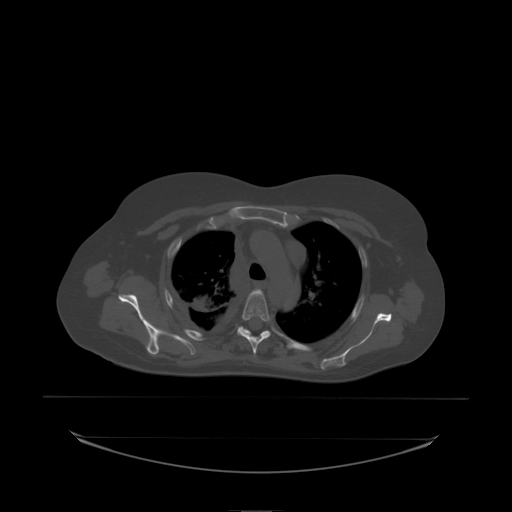
CT including the spine, one axial slice. Position 165 of 242 along the scan axis. Bone window (W 1800 / L 400 HU). 2.5 mm slice thickness. 512 × 512 image matrix, field of view 500 × 500 mm. Patient: female, 53 years. Case-level facts recorded for this patient, not image findings: primary cancer: lung.
Annotated regions visible in this slice (semi-automatically segmented with operator editing):
- T4 vertebra: bounding box <238,290,270,338> (left, top, right, bottom; pixels)
- T5 vertebra: <238,327,267,338>